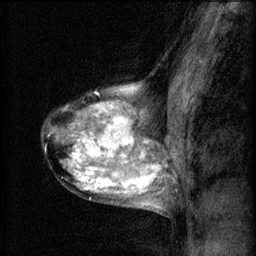
Breast MRI (dynamic contrast-enhanced), one sagittal slice; position 41 of 60 along the scan axis; 3 images stored at this slice position (order not interpretable as contrast timing); 1.5 T; TE 4.2 ms, TR 8.2 ms; 2 mm slice thickness; 256 × 256 image matrix, field of view 180 × 180 mm. Patient: female, 40 years.
Structures marked on this image (semi-automatic segmentation, software-assisted and operator-edited):
- analysis volume of interest (the breast-tissue region the enhancement analysis was run in; not a lesion): bounding box <41,80,167,211> (left, top, right, bottom; pixels)
- tumour enhancement mask (voxels above the 70 % enhancement threshold inside the analysis volume of interest): <70,86,161,207>